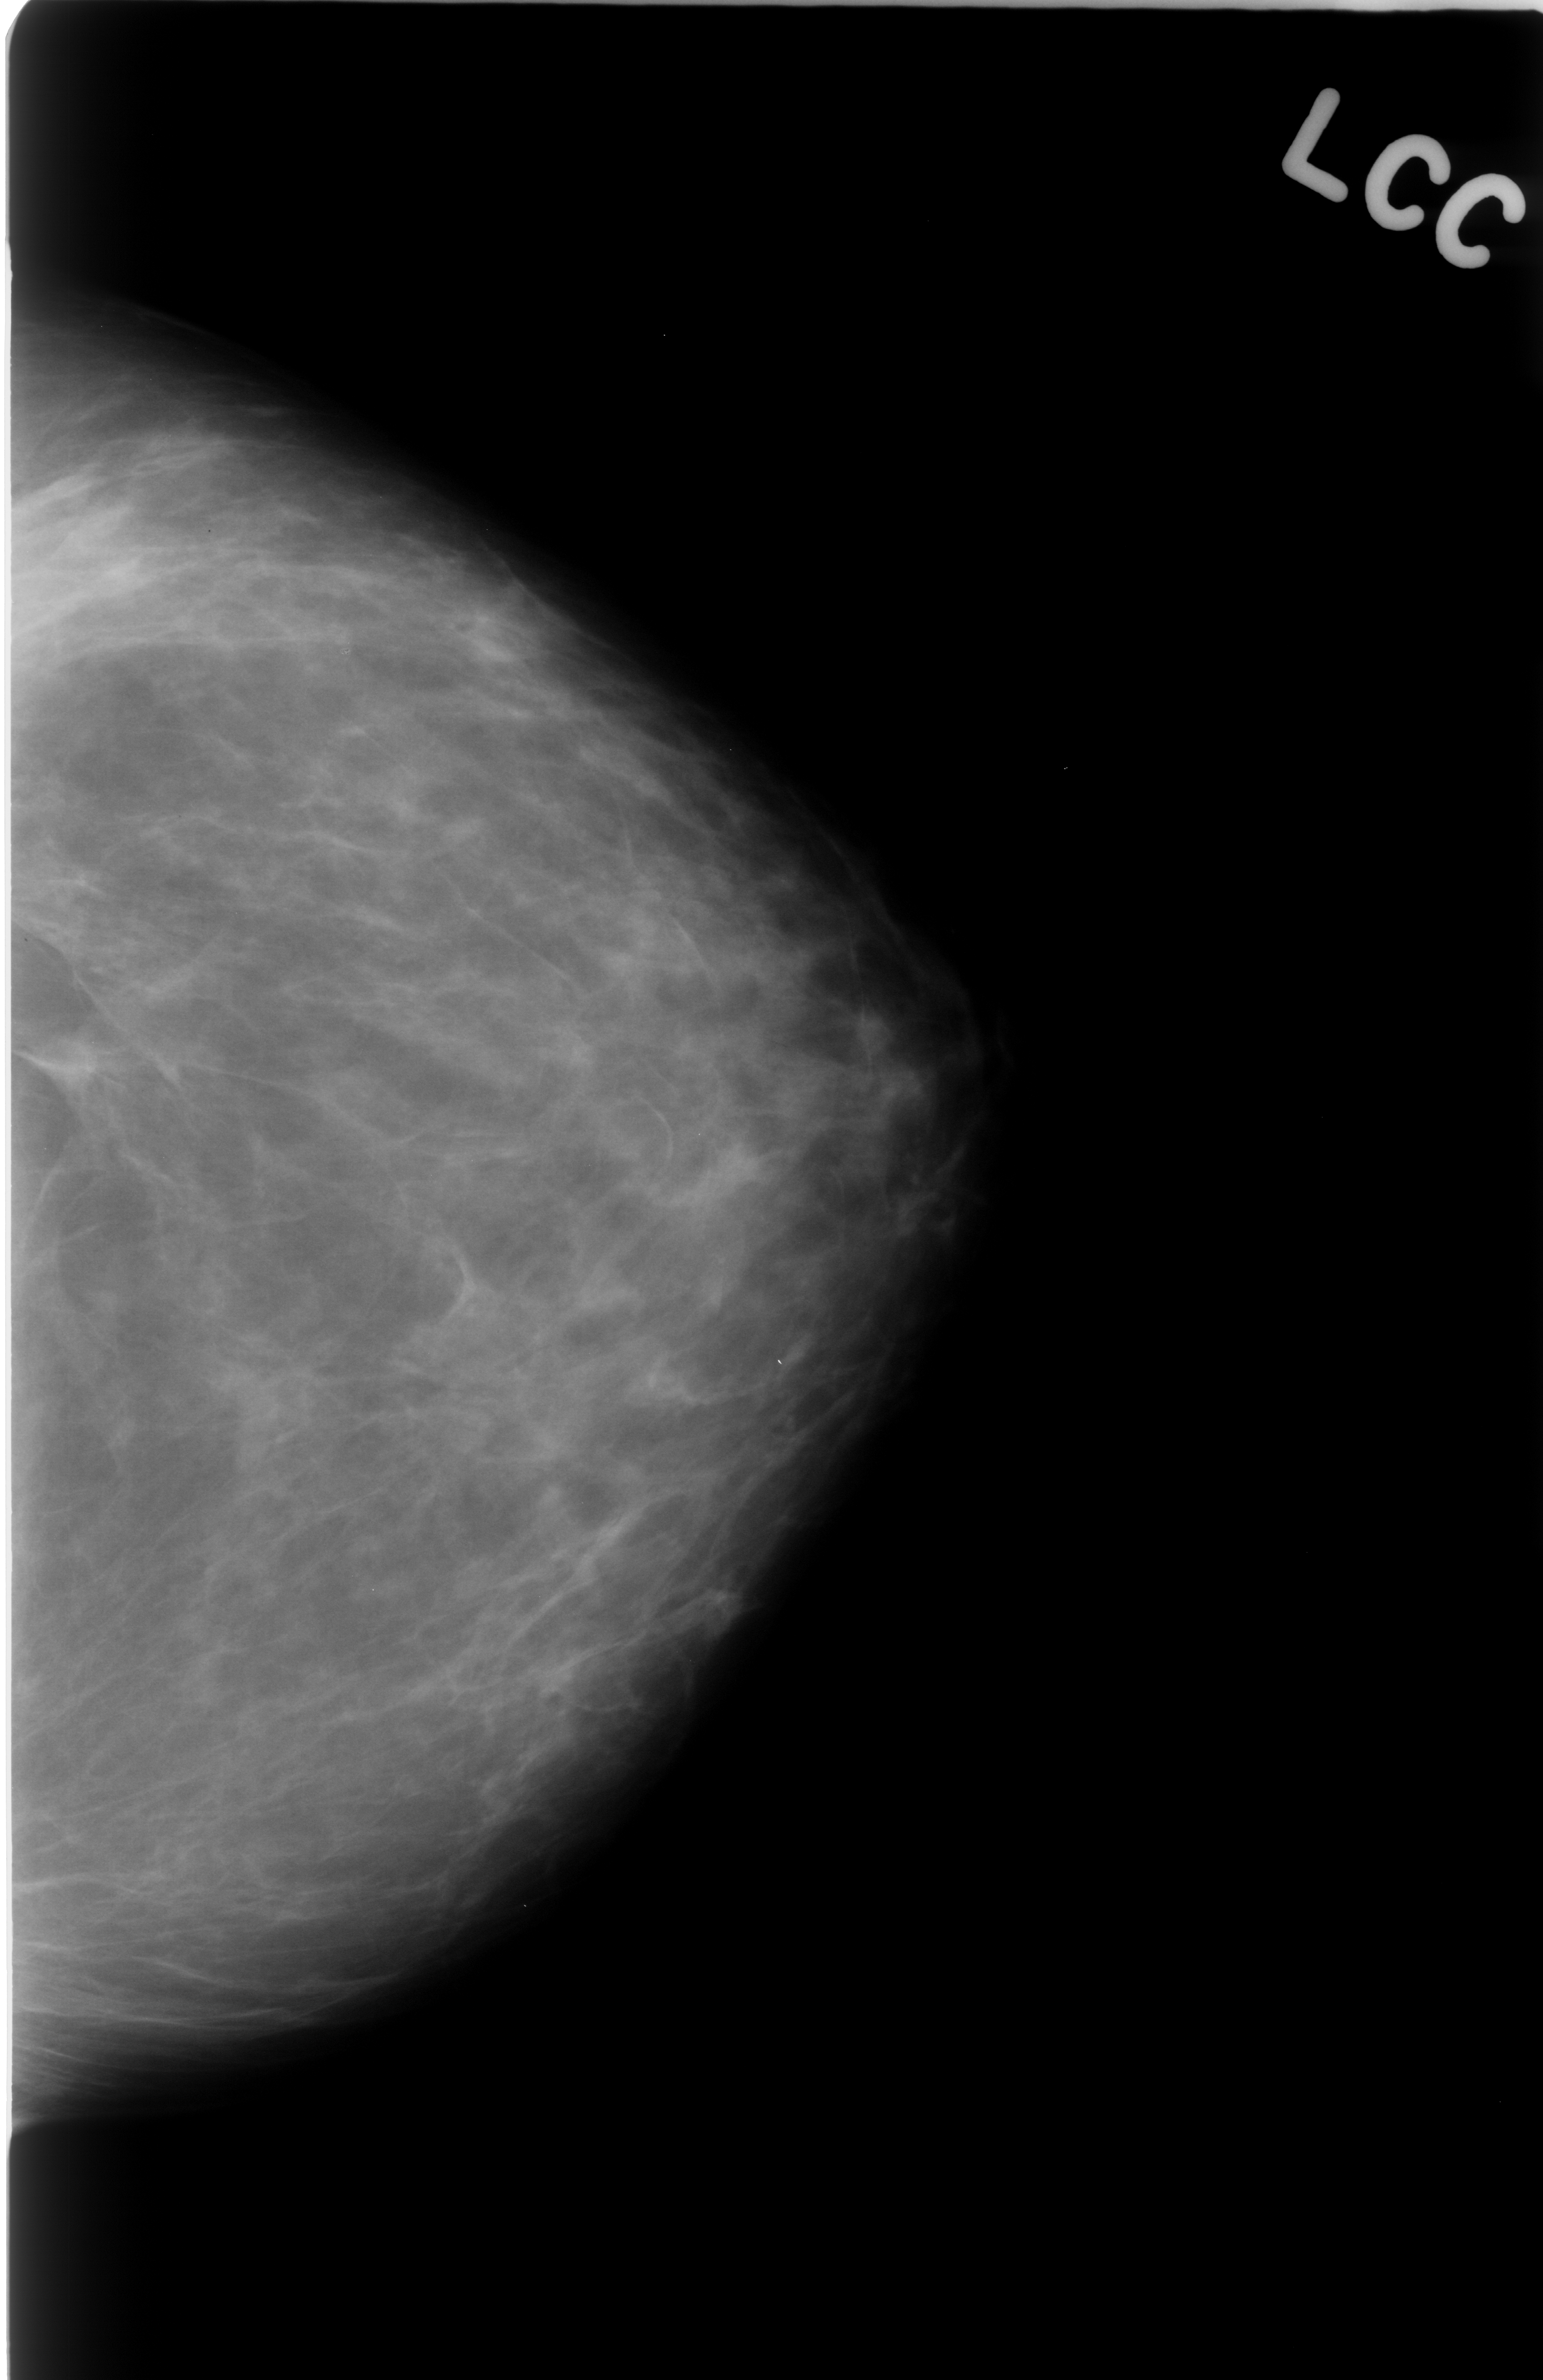
Mammogram (digitized film). Left breast. CC view. BI-RADS breast density category 1 (scale 1–4). 1543 × 2380 image matrix.
Expert-marked regions of interest on this film, with their recorded descriptors:
- mass, shape asymmetric breast tissue; BI-RADS assessment category 3; outcome (as recorded, no biopsy): benign without callback (not worked up further): bounding box <0,406,166,734> (left, top, right, bottom; pixels)